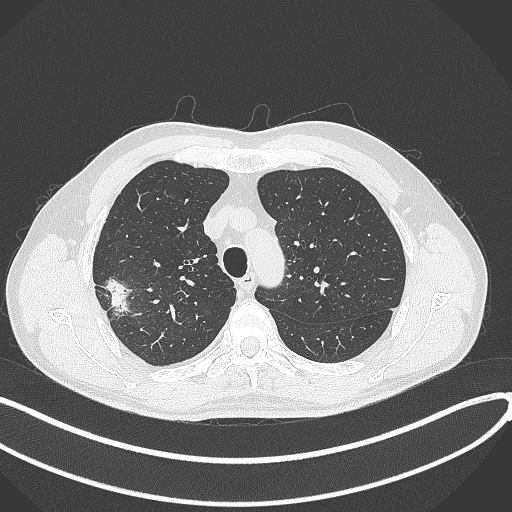
Chest CT, one axial slice. Slice 320 of 381 in the series (ordered by position). Reconstruction kernel B70f. 120 kVp. Lung window (W 1500 / L -600 HU). 1 mm slice thickness. 512 × 512 image matrix, field of view 400 × 400 mm. Male patient, age 62 years. Case-level facts recorded for this patient, not image findings: clinical TNM (as recorded): T1c N0 M0; histopathological grade: G2-3.
Structures marked on this image (bounding box drawn by a radiologist):
- lung tumour (recorded histology: adenocarcinoma): box from (x=100, y=273) to (x=134, y=318) px